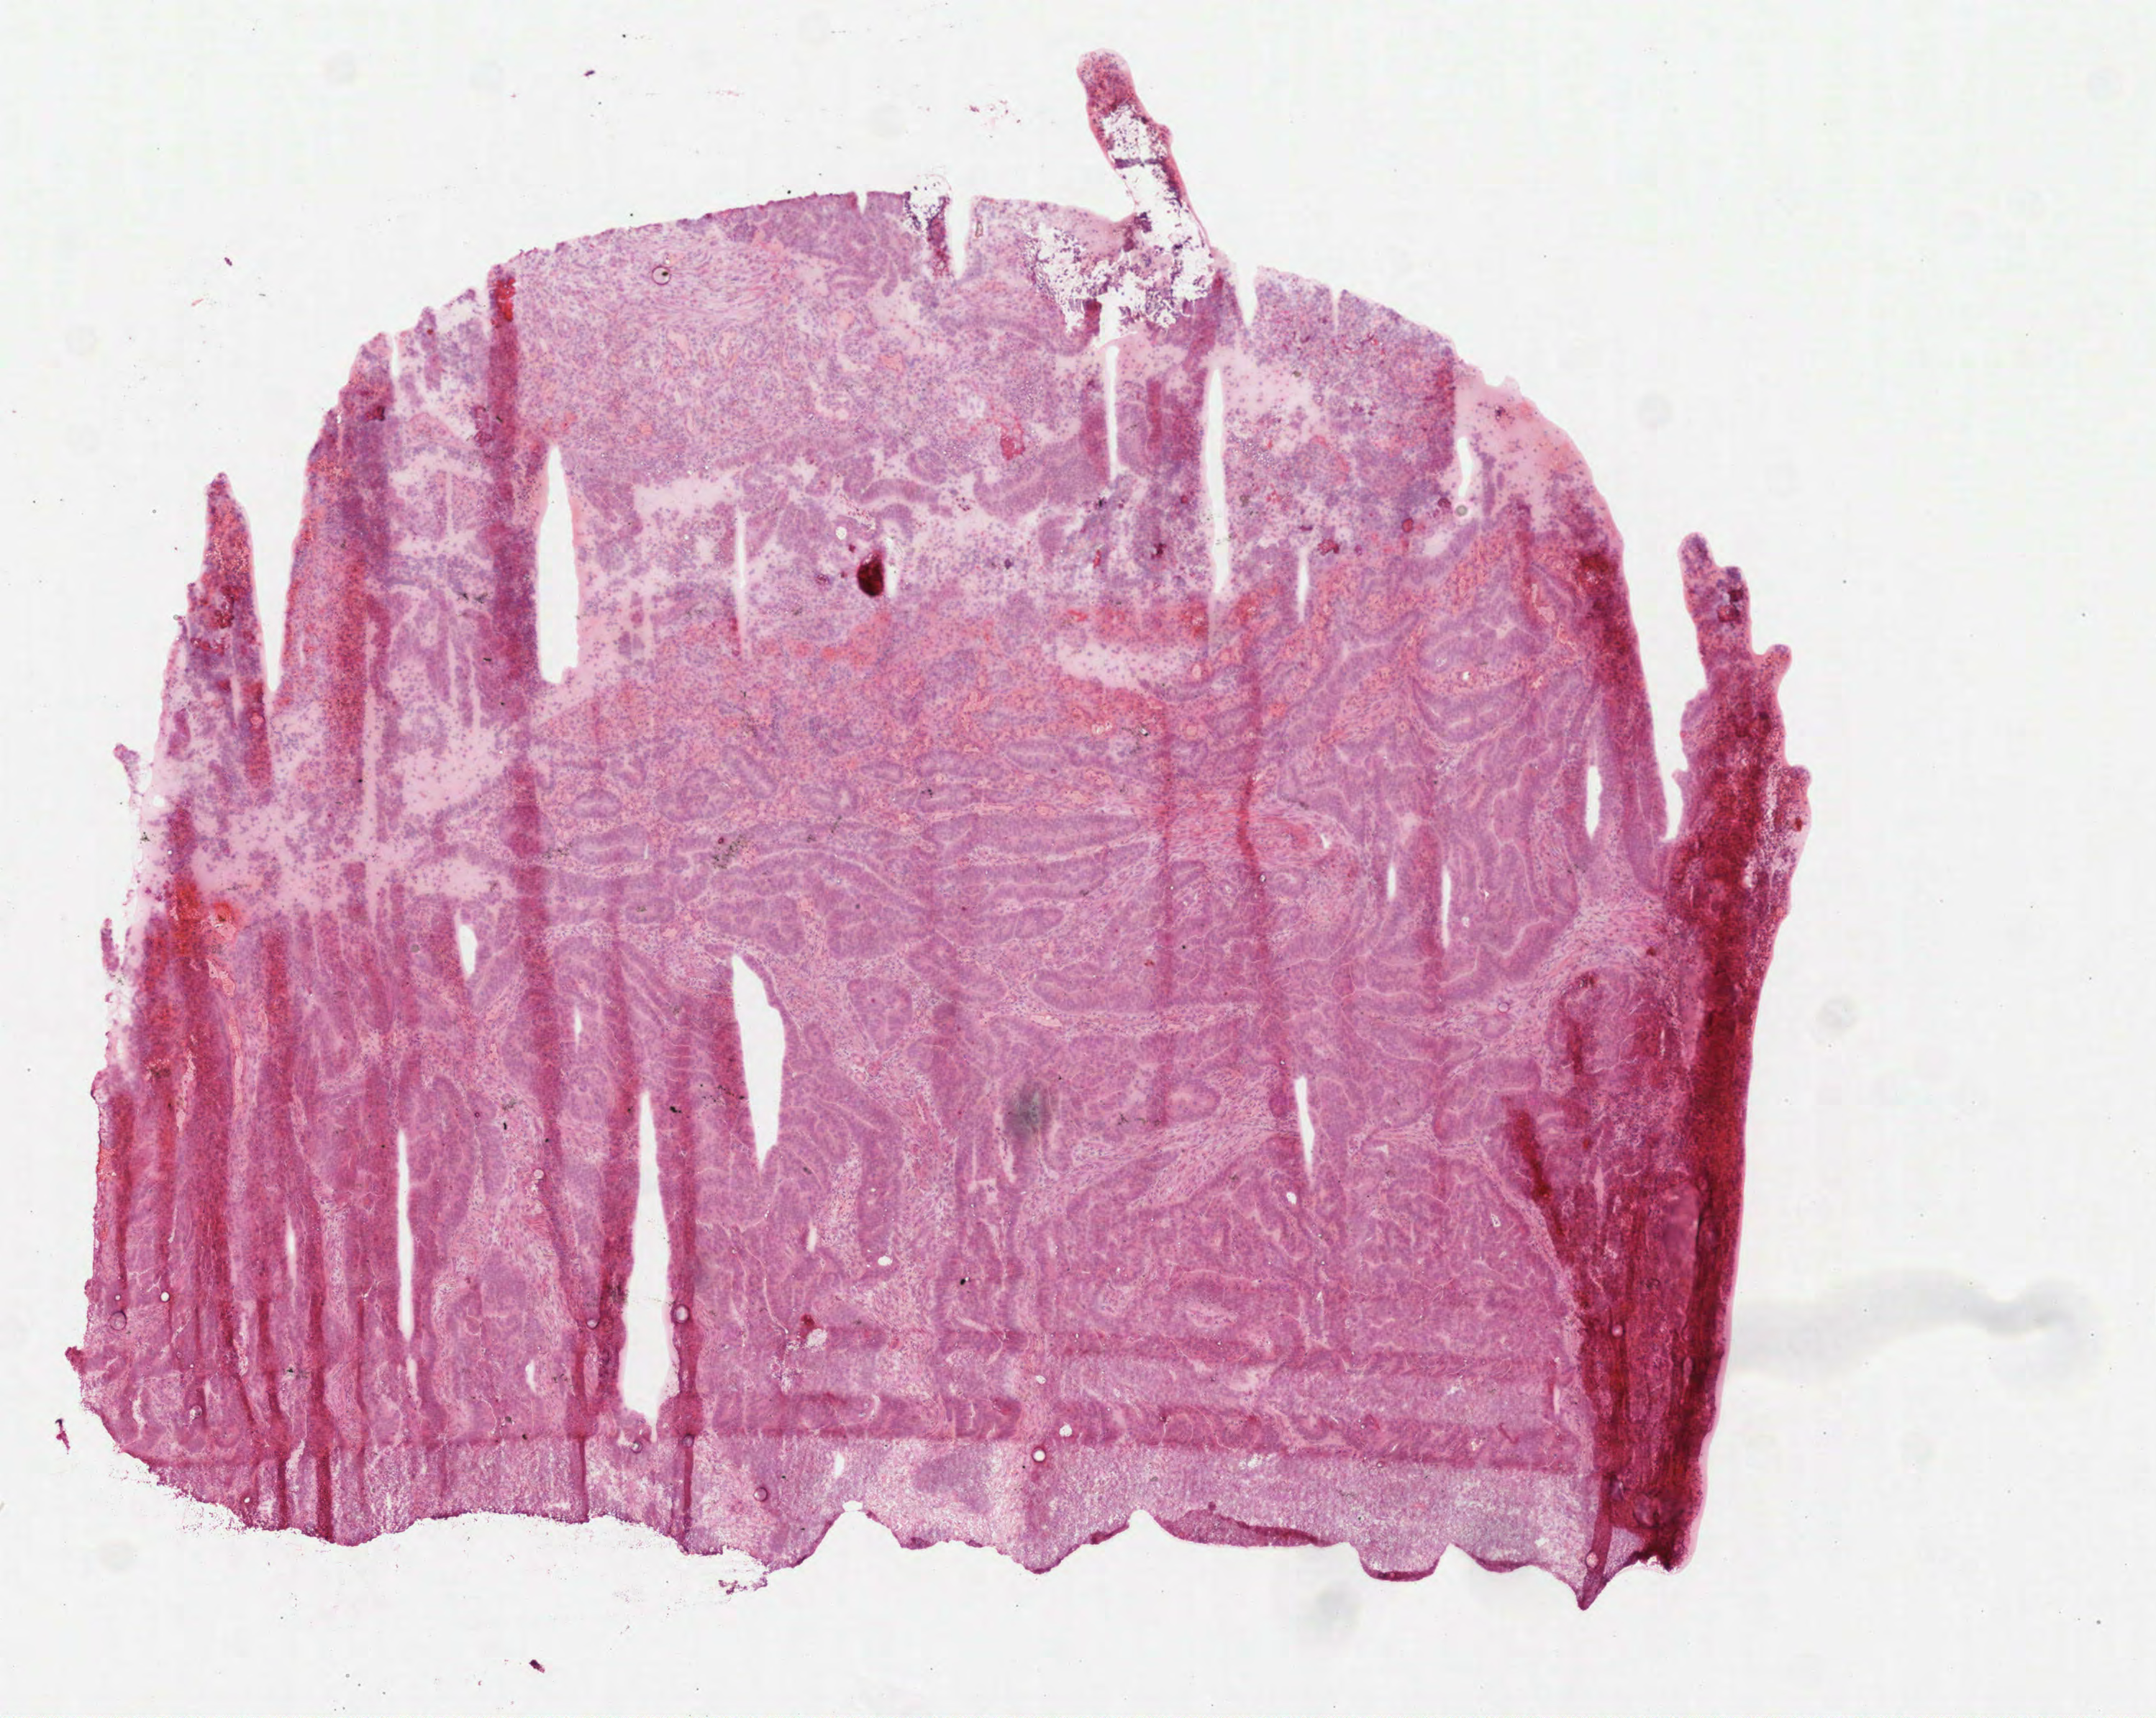
Whole-slide histology image, H&E-stained, a low-resolution overview of the entire scanned area, about 6.0 x 4.8 mm. Frozen section. Colon, primary tumour sample. Male patient; age at initial diagnosis 76 years. Pathologist review of this section (percent, as recorded): tumour cells 65%, tumour nuclei 65%, normal cells 0%, stromal cells 35%, necrosis 0%. Inflammatory infiltration, as recorded: lymphocyte infiltration 15%, monocyte infiltration 0%, neutrophil infiltration 0%.
Histologic diagnosis: Adenocarcinoma, NOS (sigmoid colon). AJCC pathologic stage: IIIA. Lymph nodes positive (case pathology): 1 of 8 examined.